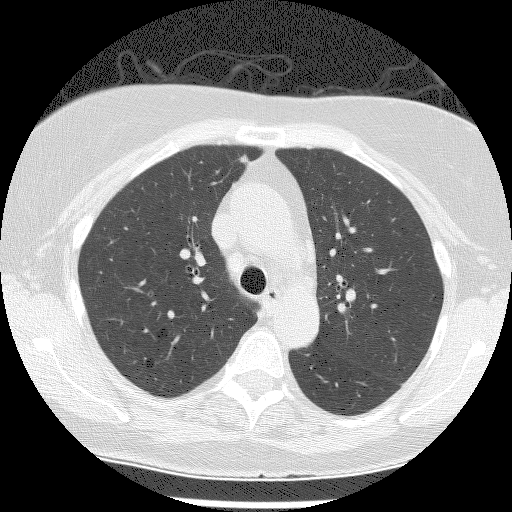
Low-dose screening chest CT, one axial slice; position 103 of 149 along the scan axis; reconstruction kernel BONE; 120 kVp; lung window (W 1500 / L -600 HU); 2.5 mm slice thickness; 512 × 512 image matrix, field of view 300 × 300 mm.
Outlined on this slice (expert manual segmentation):
- lesion 1 (tumor, upper lobe of right lung): box from (x=238, y=154) to (x=250, y=165) px